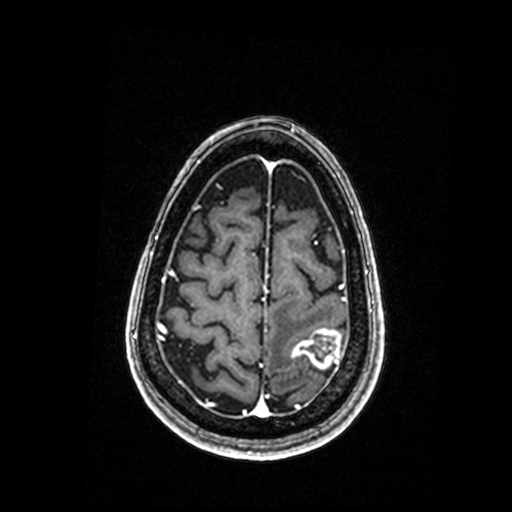
Brain MRI from a brain-tumour surgery series, one axial slice; slice 46 of 192 in the series (ordered by position); T1-weighted post-contrast; 0.98 mm slice thickness; 512 × 512 image matrix. Case-level facts recorded for this patient, not image findings: histopathology: Metastastic Carcinoma, Poorly Differentiated.
Outlined on this slice (manually delineated by an expert):
- tumour: bounding box (x1, y1, x2, y2) in pixels: (293, 329, 341, 369)